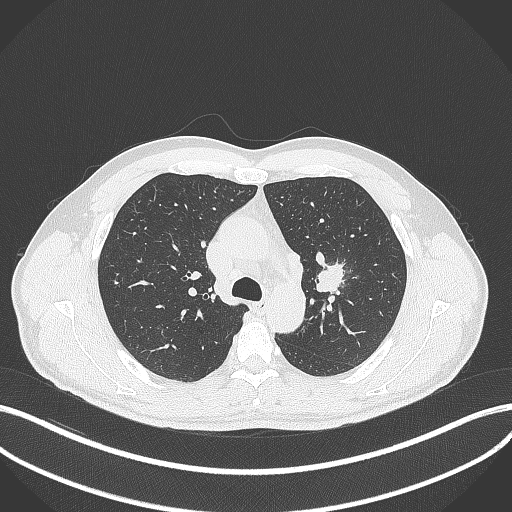
Chest CT, one axial slice; slice 292 of 392 in the series (ordered by position); reconstruction kernel B70f; 120 kVp; lung window (W 1500 / L -600 HU); 512 × 512 image matrix, field of view 400 × 400 mm. Male patient, age 50 years. Case-level facts recorded for this patient, not image findings: clinical TNM (as recorded): T1c N1 M1b.
Structures marked on this image (bounding box drawn by a radiologist):
- lung tumour (recorded histology: squamous cell carcinoma): bounding box [x1, y1, x2, y2] px = [313, 257, 347, 295]